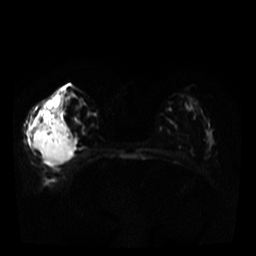
Breast MRI, one axial slice; slice 15 of 34 in the series (ordered by position); diffusion-weighted series; image 2 of 4 stored at this slice position (different b-values; order by instance number); 3 T; 5 mm slice thickness; 256 × 256 image matrix. Female patient.
Annotated regions visible in this slice (manually delineated by an expert):
- tumour on diffusion-weighted imaging: bounding box [x1, y1, x2, y2] px = [34, 123, 73, 161]